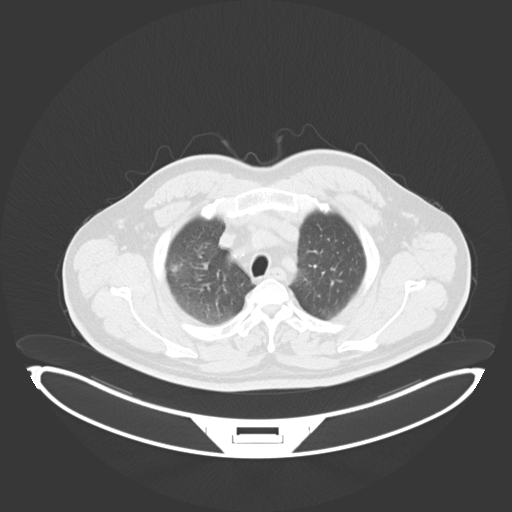
Chest CT, one axial slice. Position 230 of 284 along the scan axis. Reconstruction kernel B30f. 120 kVp. Lung window (W 1500 / L -600 HU). 3 mm slice thickness. 512 × 512 image matrix. Patient: male, 55 years. From the clinical record (not read from this slice): clinical TNM (as recorded): T3 N2 M1.
Outlined on this slice (rectangle marked by the reading radiologist):
- lung tumour (recorded histology: adenocarcinoma): bounding box (x1, y1, x2, y2) in pixels: (168, 258, 186, 274)